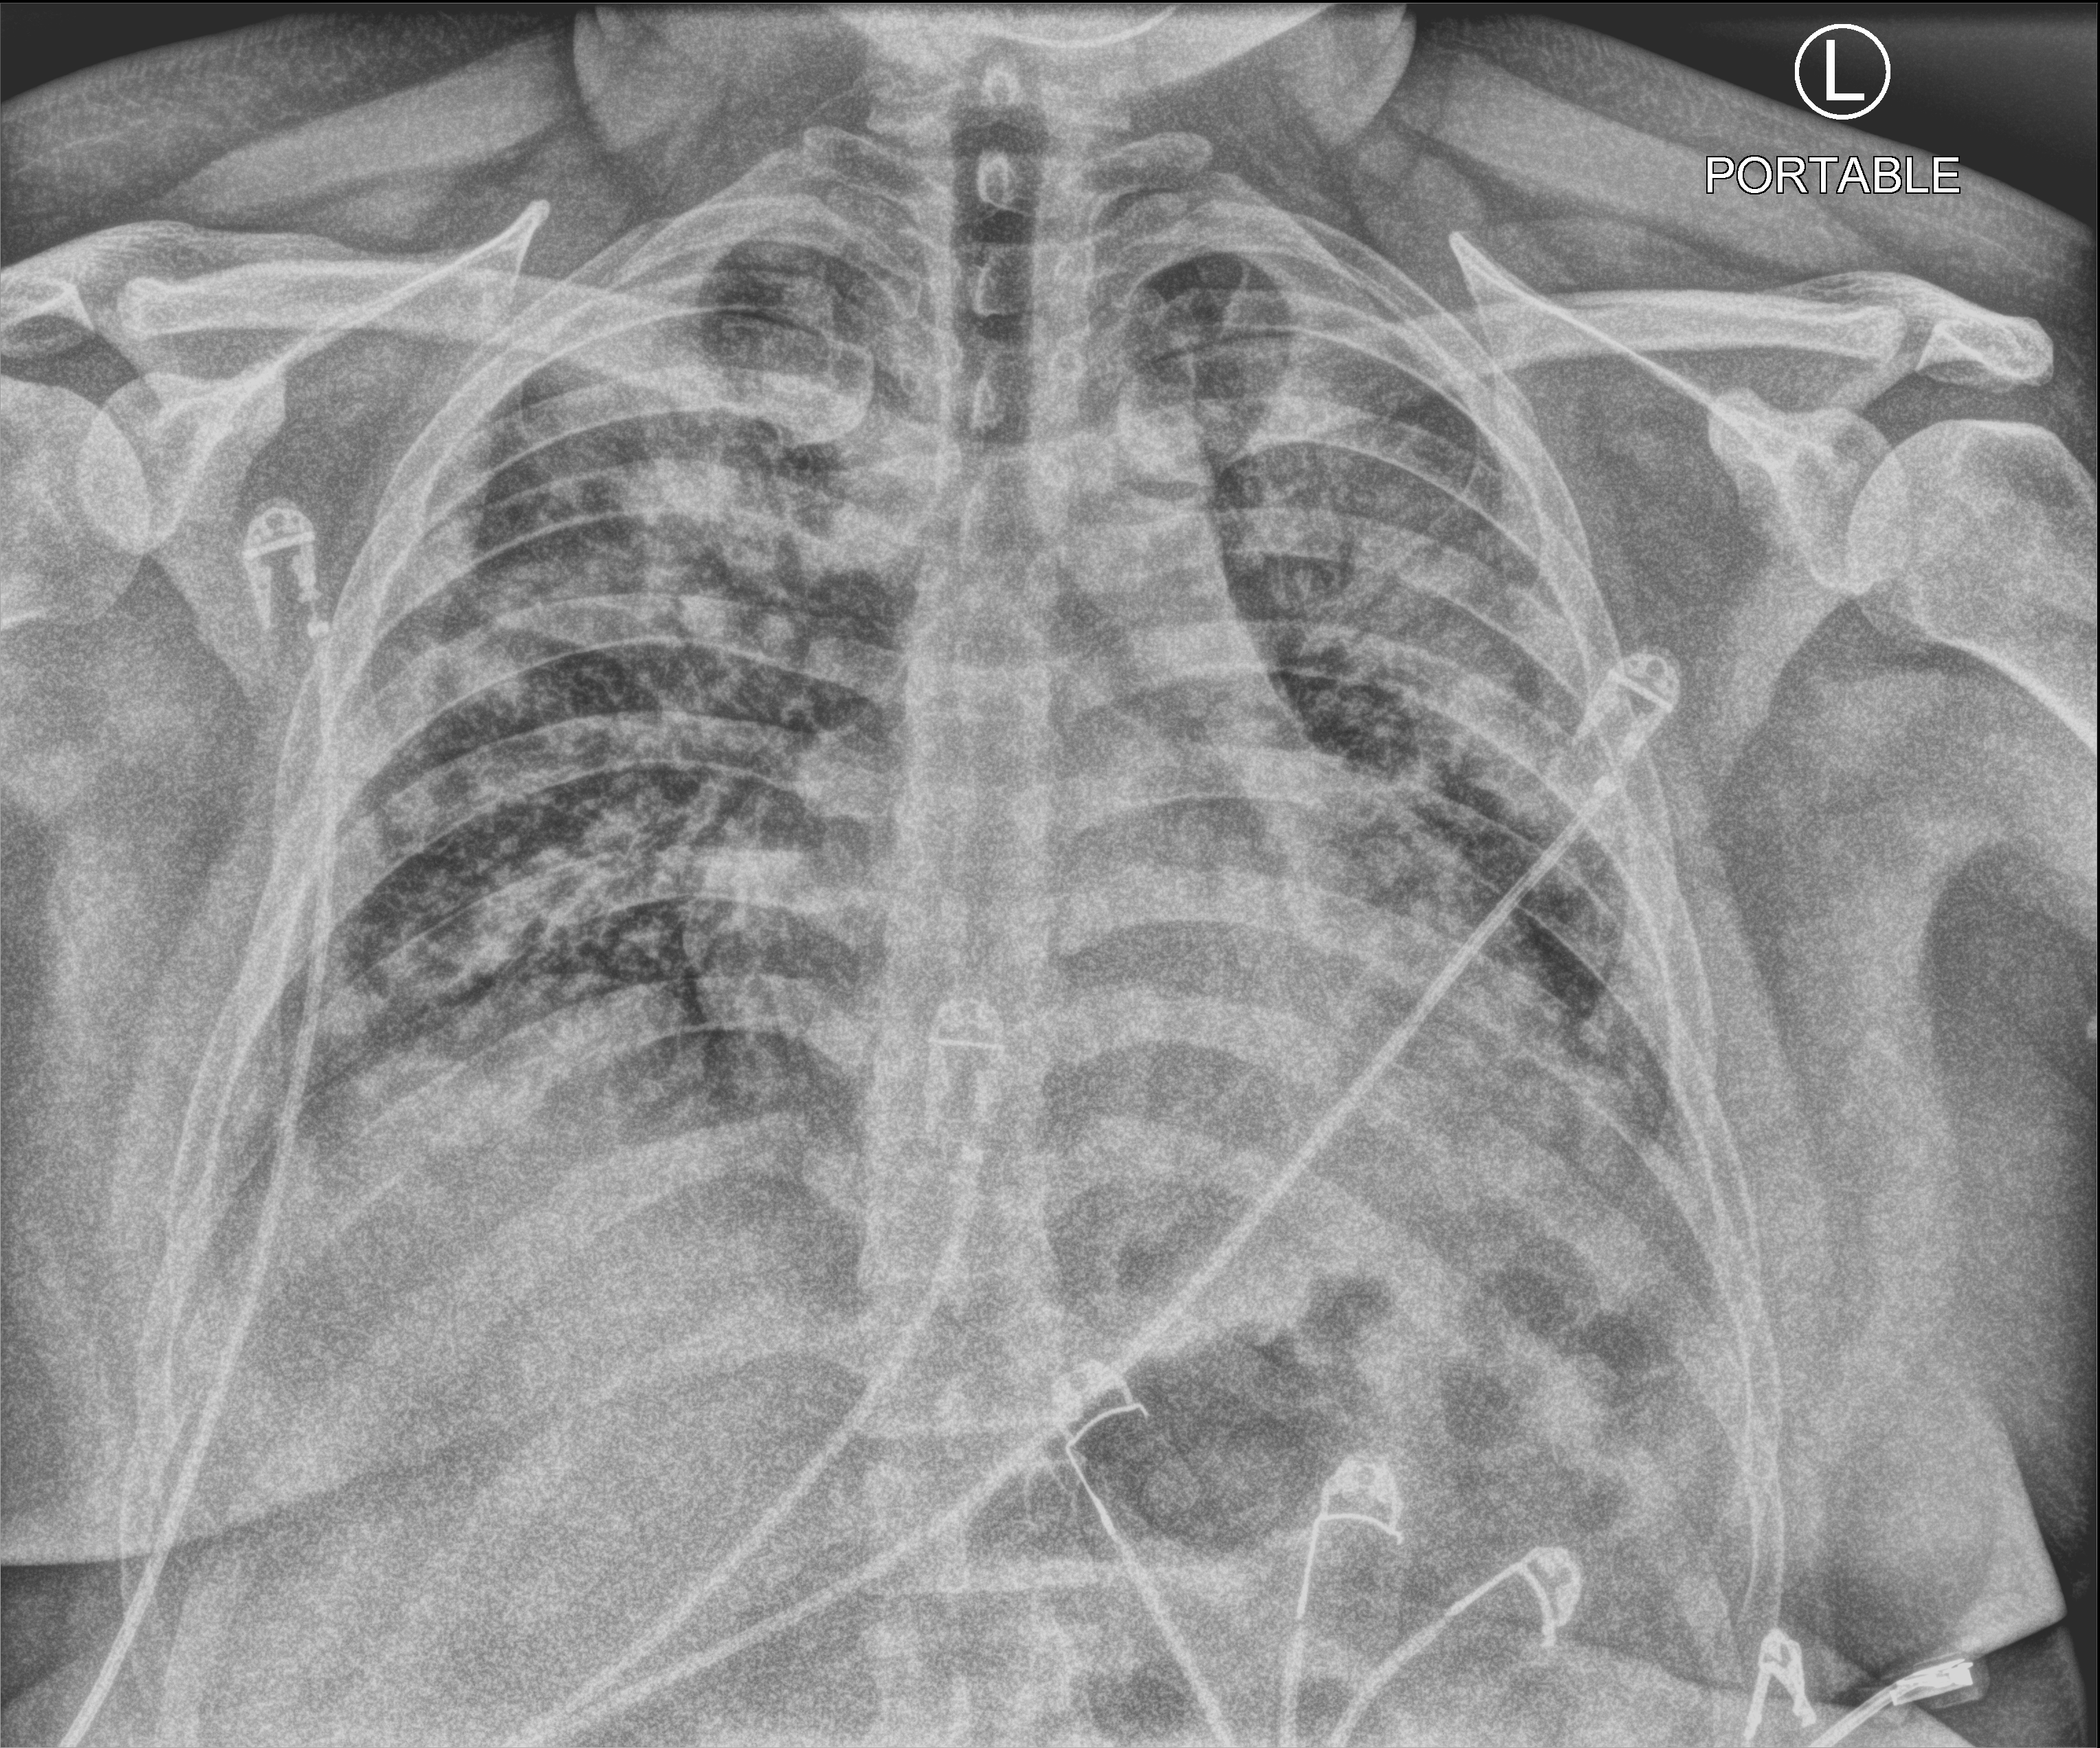
Chest X-ray (portable); anteroposterior (AP) projection. Patient hospitalised with COVID-19; male, aged 18–59 years.
Hospital-stay facts (about this admission, not read from this image; timing relative to this image not recorded):
- admitted to intensive care during this hospital stay: no